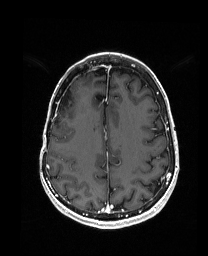
Brain MRI from a brain-tumour surgery series, one axial slice. Position 60 of 192 along the scan axis. T1-weighted post-contrast. 1 mm slice thickness. 208 × 256 image matrix, field of view 203 × 250 mm. Case-level facts recorded for this patient, not image findings: histopathology: Metastatic Carcinoma from Breast primary; tumour location: Right Frontal.
Outlined on this slice (expert manual segmentation):
- previous resection cavity: box from (x=61, y=86) to (x=72, y=105) px